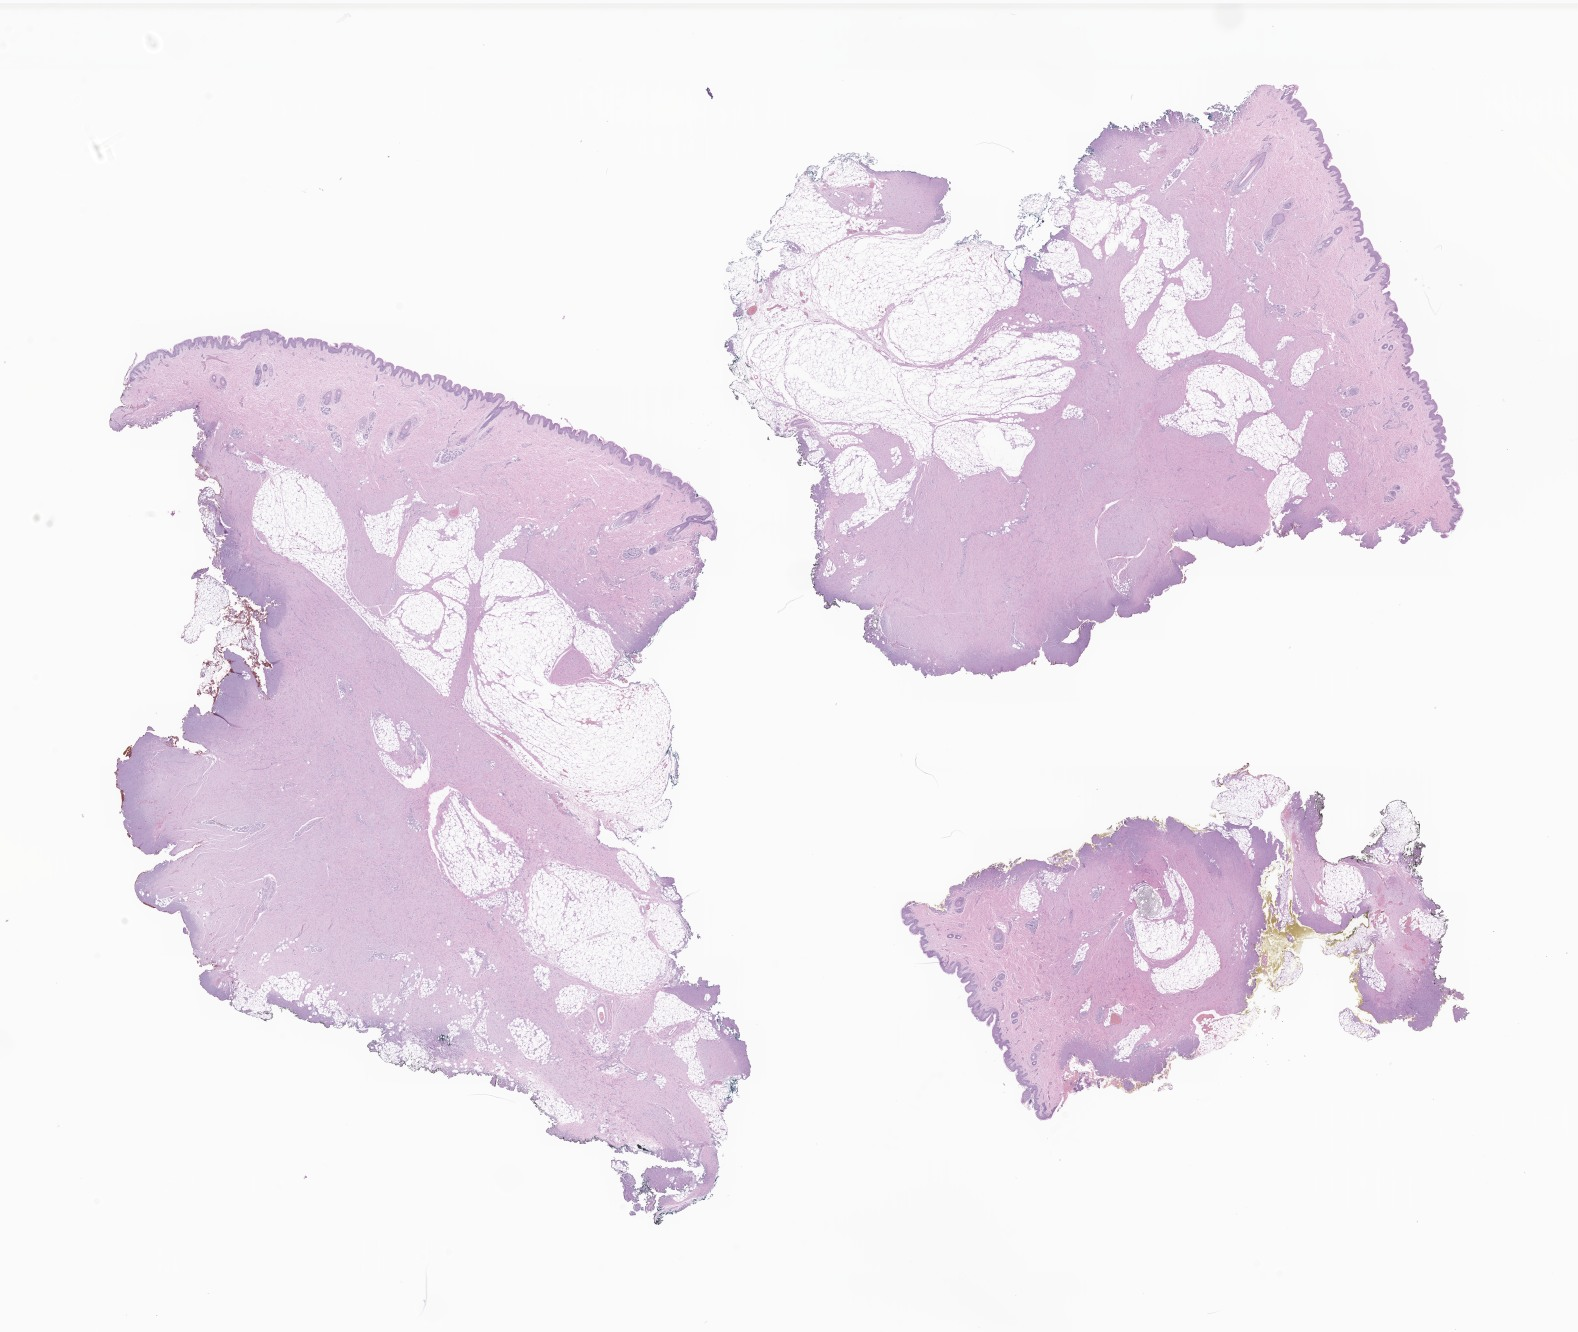
Digitized hematoxylin and eosin (H&E)-stained section of tumor tissue from the soft tissue of upper extremity — shown as a low-resolution overview of the whole scanned area (about 26.6 x 22.5 mm); formalin-fixed paraffin-embedded section. Male patient, age 502 days (about 1.4 years).
Diagnosis: Myofibroblastic tumor, NOS.